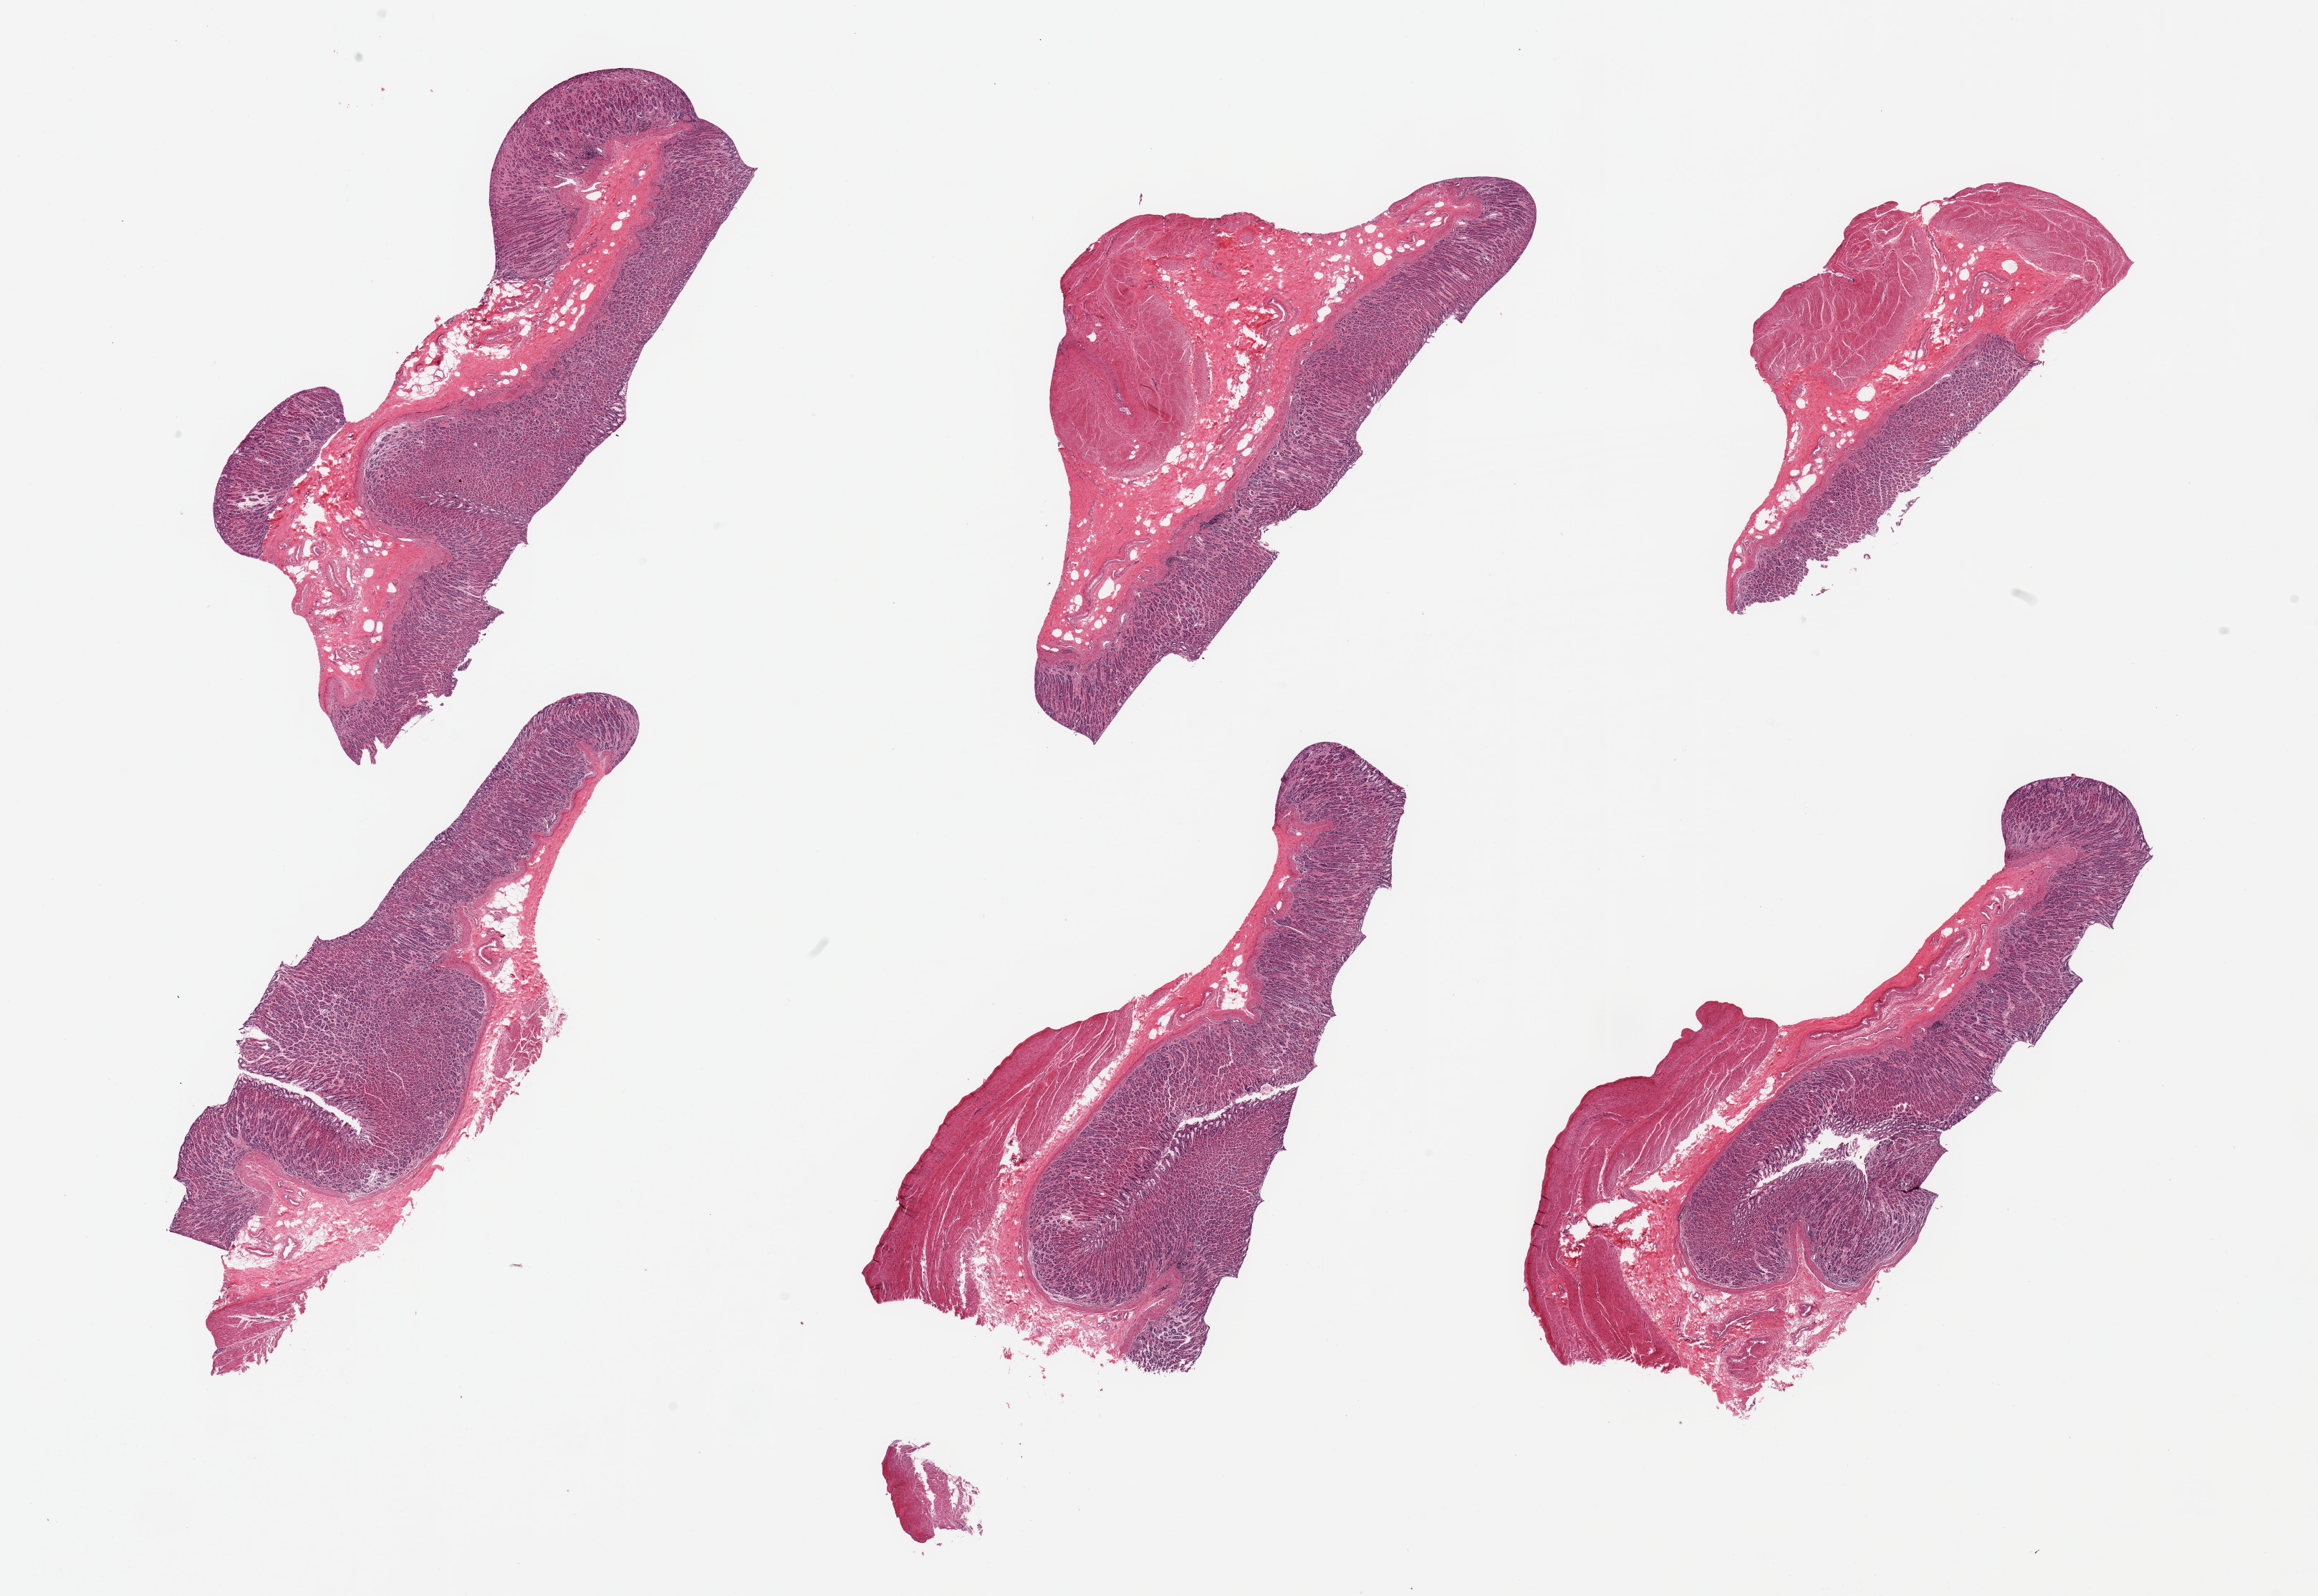
Whole-slide image, hematoxylin and eosin (H&E) stain, shown as a low-resolution overview of the whole scanned area (about 25.6 x 17.6 mm, from a 20x scan); PAXgene-fixed paraffin-embedded (PFPE) section; sampled site (target tissue): stomach; tissue donor sample. Male donor.
Reviewer comment on this tissue sample: 6 pieces, mucosa up to ~1mm, 30-90% of thickness.